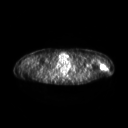
FDG PET of an extremity soft-tissue mass (from a PET/CT study), one axial slice. Slice 202 of 267 in the series (ordered by position). 3.27 mm slice thickness. 128 × 128 image matrix. Female patient, age 28 years. From the clinical record (not read from this slice): histological type: malignant fibrous histiocytoma; grade: low; site of the primary tumour: left arm.
Annotated regions visible in this slice (expert contour drawn on MRI and transferred to this co-registered scan by the dataset authors):
- gross tumour volume (mass): bounding box [x1, y1, x2, y2] px = [99, 62, 106, 69]